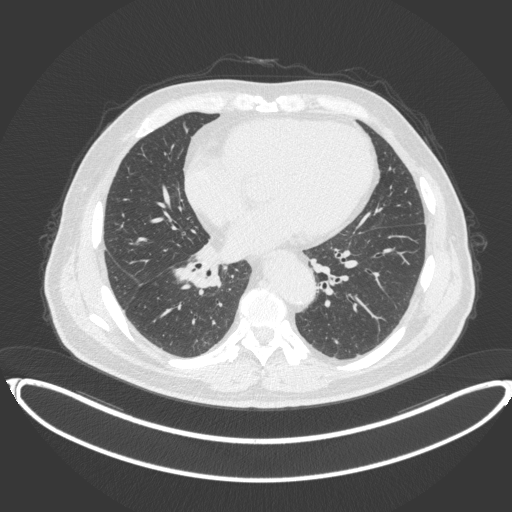
Chest CT, one axial slice. Slice 170 of 383 in the series (ordered by position). Reconstruction kernel B31f. 120 kVp. Lung window (W 1500 / L -600 HU). 1 mm slice thickness. 512 × 512 image matrix, field of view 448 × 448 mm. Male patient, age 61 years. Case-level facts recorded for this patient, not image findings: clinical TNM (as recorded): T1b N1 M0.
Structures marked on this image (bounding box drawn by a radiologist):
- lung tumour (recorded histology: squamous cell carcinoma): box from (x=170, y=255) to (x=224, y=293) px